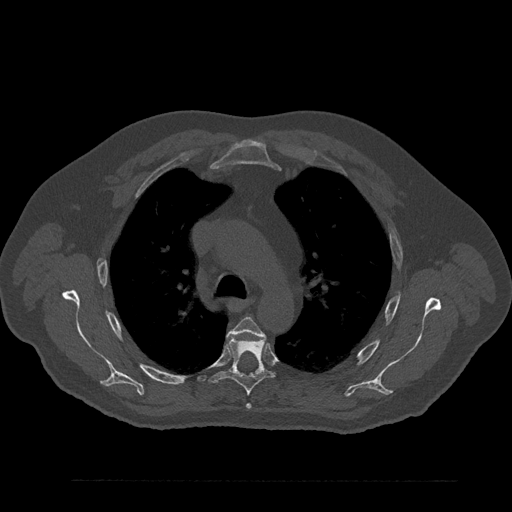
CT including the spine, one axial slice; position 609 of 797 along the scan axis; bone window (W 1800 / L 400 HU); 0.5 mm slice thickness; 512 × 512 image matrix, field of view 430 × 430 mm. Patient: male, 61 years. Case-level facts recorded for this patient, not image findings: primary cancer: prostate.
Structures marked on this image (semi-automatically segmented with operator editing):
- T4 vertebra: bounding box [x1, y1, x2, y2] px = [229, 317, 266, 409]
- T5 vertebra: [208, 338, 274, 396]